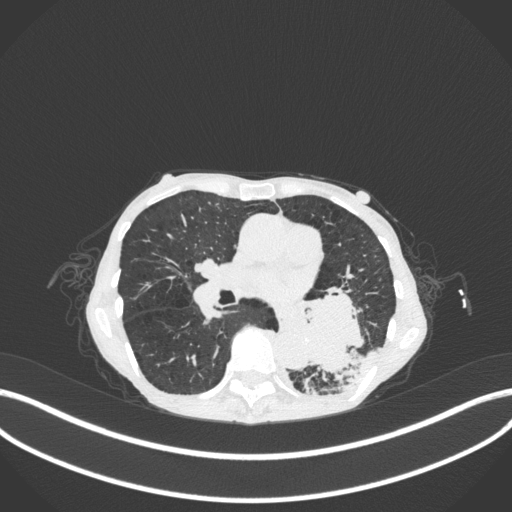
Chest CT, one axial slice; slice 139 of 347 in the series (ordered by position); reconstruction kernel B31f; 120 kVp; lung window (W 1500 / L -600 HU); 512 × 512 image matrix. Female patient, age 70 years. From the clinical record (not read from this slice): clinical TNM (as recorded): T3 N0 M0; histopathological grade: G3.
Structures marked on this image (rectangle marked by the reading radiologist):
- lung tumour (recorded histology: small cell carcinoma): box from (x=290, y=283) to (x=365, y=379) px